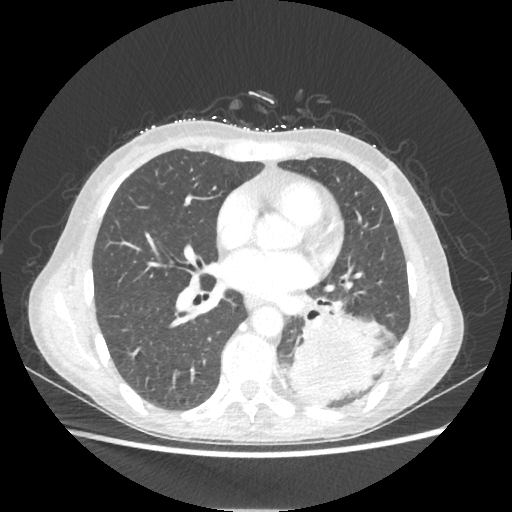
Chest CT, one axial slice. Position 103 of 221 along the scan axis. 80 kVp. Lung window (W 1500 / L -600 HU). 1.25 mm slice thickness. 512 × 512 image matrix, field of view 360 × 360 mm. Patient: female, 53 years. From the clinical record (not read from this slice): clinical TNM (as recorded): T3 N0 M0.
Annotated regions visible in this slice (rectangle marked by the reading radiologist):
- lung tumour (recorded histology: adenocarcinoma): bounding box <284,313,385,408> (left, top, right, bottom; pixels)